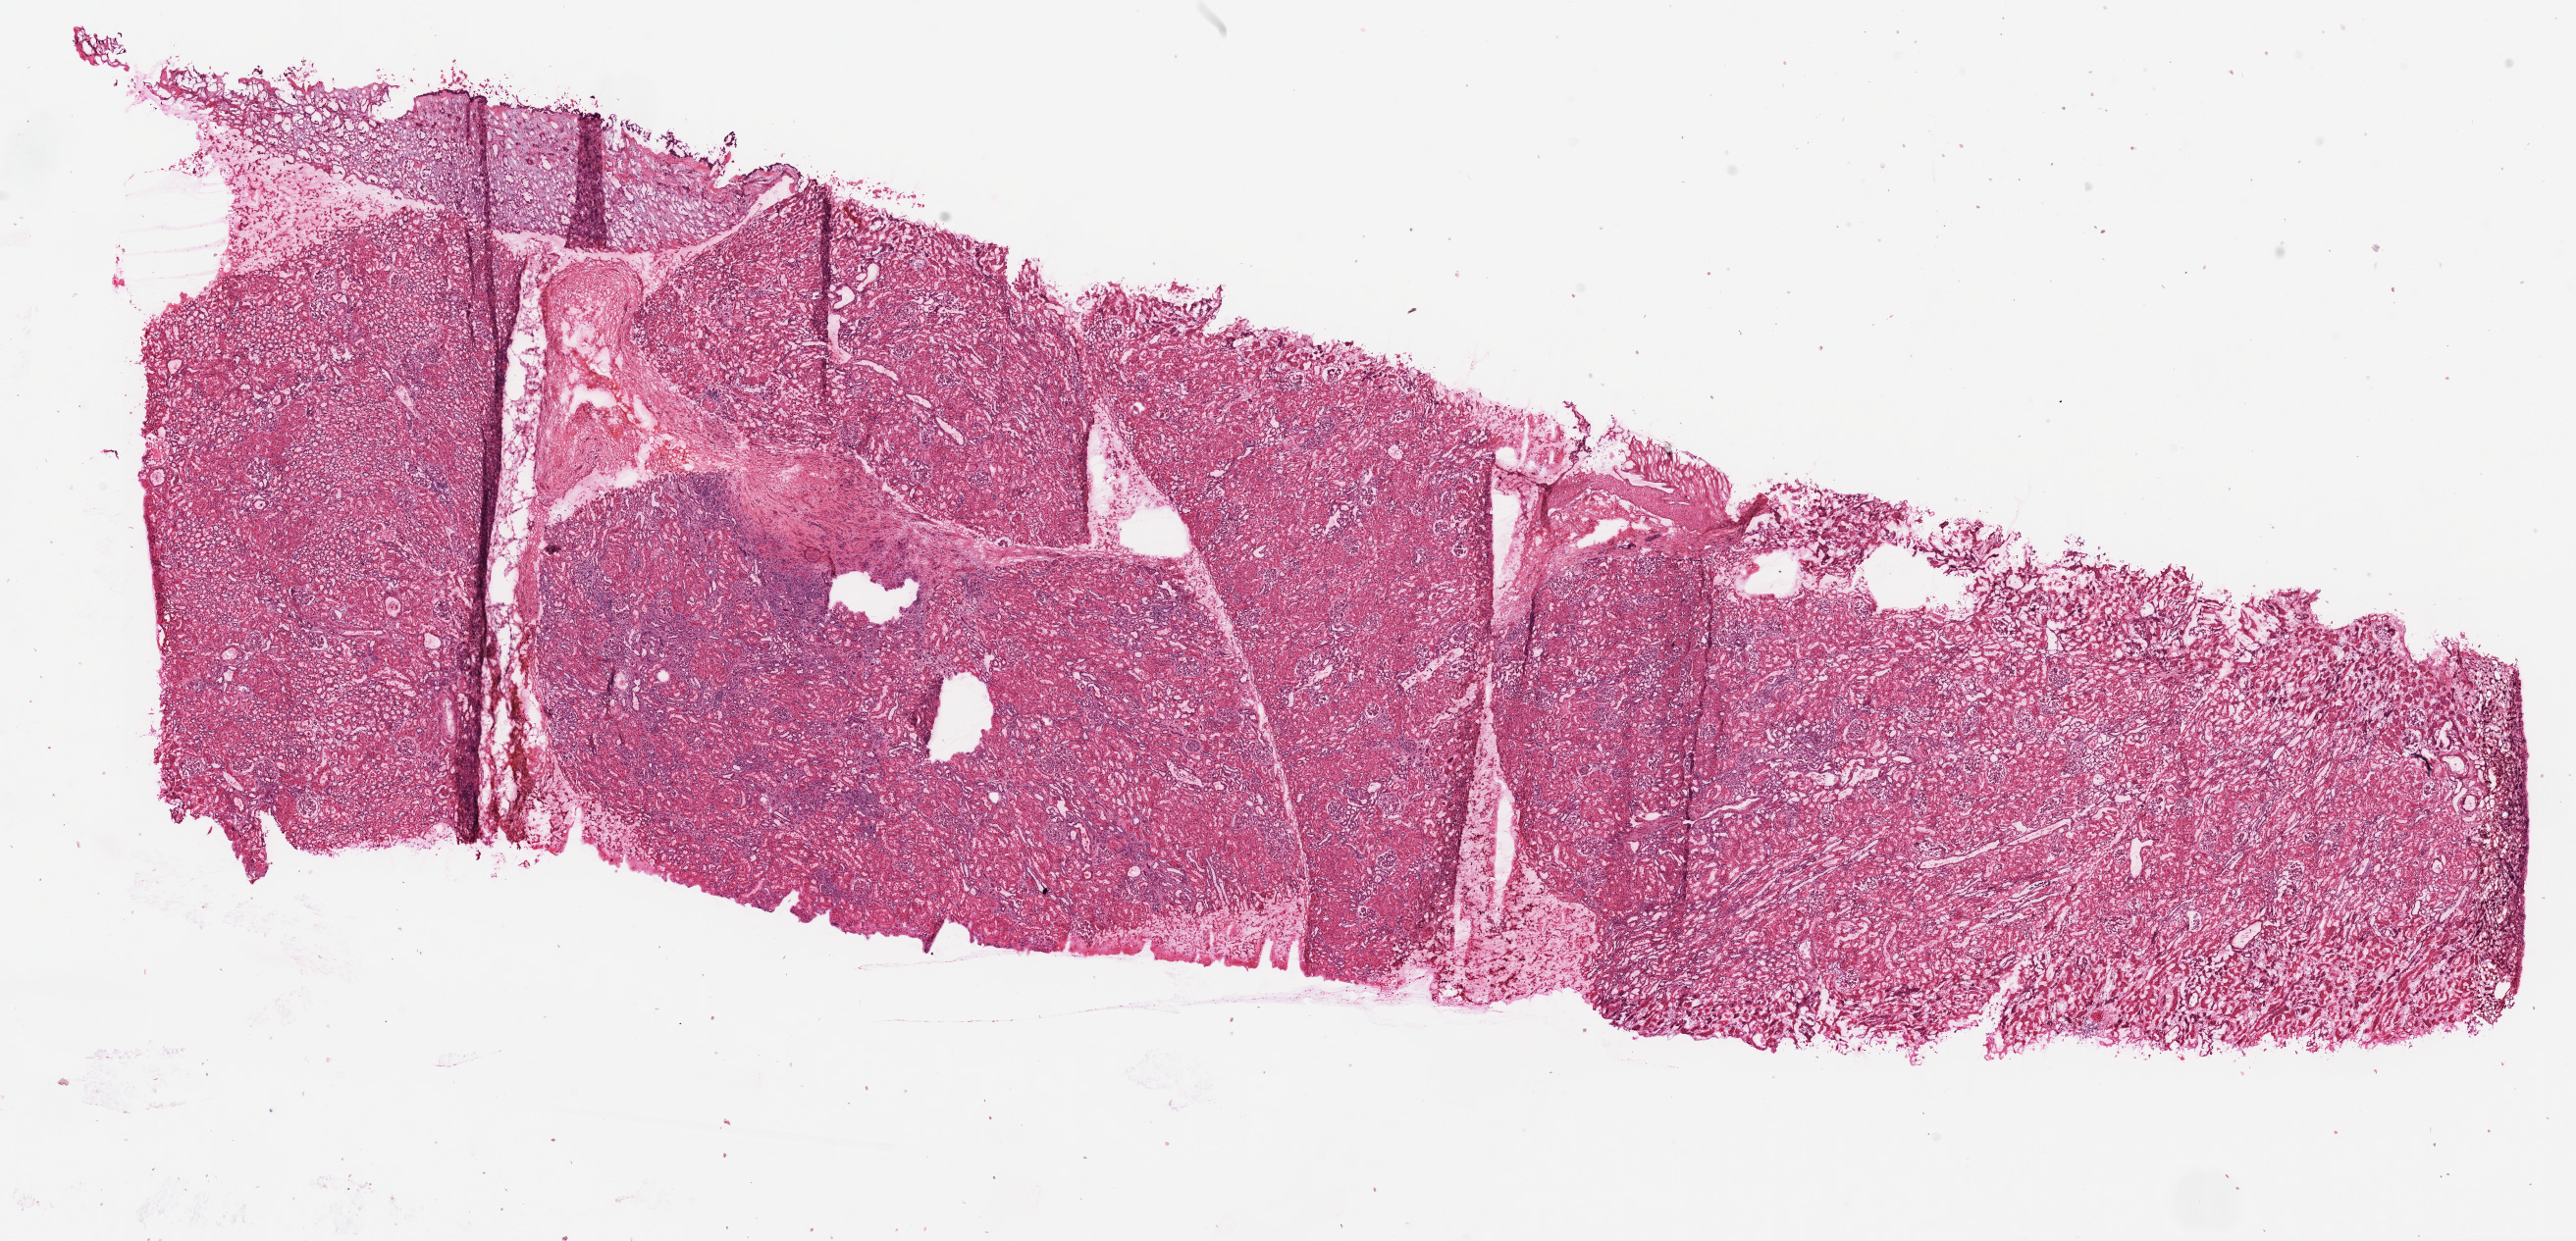
Whole-slide histology image, Hematoxylin and eosin (H&E) stained — low-resolution overview of the scanned area, about 21.1 x 10.2 mm (from a 20x scan). Frozen section from the top of the tissue portion. Kidney, solid tissue normal (non-tumour tissue) sample. Female, age 60 years at initial diagnosis.
- this section: solid tissue normal sample (biorepository sample class)
- patient diagnosis: Clear cell adenocarcinoma, NOS